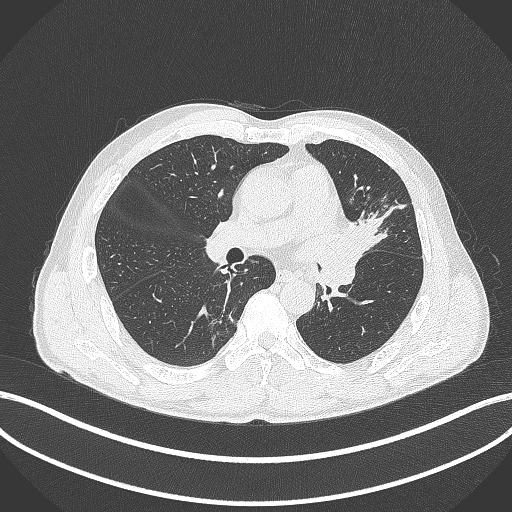
Chest CT, one axial slice; slice 232 of 429 in the series (ordered by position); 120 kVp; lung window (W 1500 / L -600 HU); 1 mm slice thickness; 512 × 512 image matrix, field of view 400 × 400 mm. Patient: male, 57 years. From the clinical record (not read from this slice): clinical TNM (as recorded): T2b N0 M0.
Annotated regions visible in this slice (bounding box drawn by a radiologist):
- lung tumour (recorded histology: squamous cell carcinoma): box from (x=331, y=213) to (x=385, y=282) px